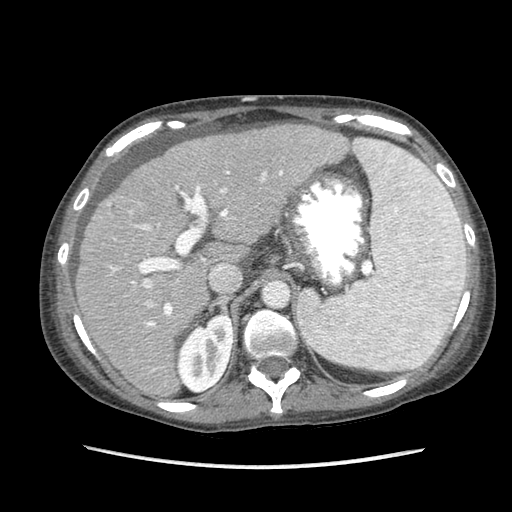
Contrast-enhanced abdominal CT (liver protocol), one axial slice. Slice 58 of 87 in the series (ordered by position). Reconstruction kernel STANDARD. 120 kVp. Soft-tissue window (W 400 / L 40 HU). 2.5 mm slice thickness. 512 × 512 image matrix, field of view 340 × 340 mm. From the clinical record (not read from this slice): diagnosis: hepatocellular carcinoma (patient treated with transarterial chemoembolisation; whether this scan precedes or follows treatment is not stated here); TNM stage (as recorded): Stage-IIIB; Child-Pugh class: A; tumour differentiation: no biopsy; tumour nodularity: uninodular.
Structures marked on this image (semi-automatic segmentation, software-assisted and operator-edited):
- abdominal aorta: box from (x=264, y=281) to (x=289, y=307) px
- liver parenchyma outside the tumour (the mass and vessels are separate outlines, so this box may not span the whole liver): (x=76, y=123)–(x=350, y=396)
- mass: (x=106, y=194)–(x=137, y=225)
- liver vessels: (x=108, y=170)–(x=283, y=372)